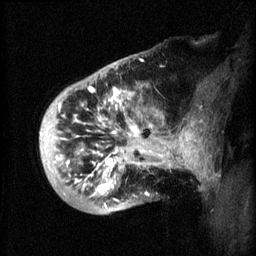
Breast MRI (dynamic contrast-enhanced), one sagittal slice; position 12 of 60 along the scan axis; 3 images stored at this slice position (order not interpretable as contrast timing); 1.5 T; TE 4.2 ms, TR 8.2 ms; 2 mm slice thickness; 256 × 256 image matrix, field of view 200 × 200 mm. Female patient, age 50 years.
Annotated regions visible in this slice (semi-automatically segmented with operator editing):
- analysis volume of interest (the breast-tissue region the enhancement analysis was run in; not a lesion): bounding box [x1, y1, x2, y2] px = [44, 72, 173, 215]
- tumour enhancement mask (voxels above the 70 % enhancement threshold inside the analysis volume of interest): [46, 86, 173, 209]